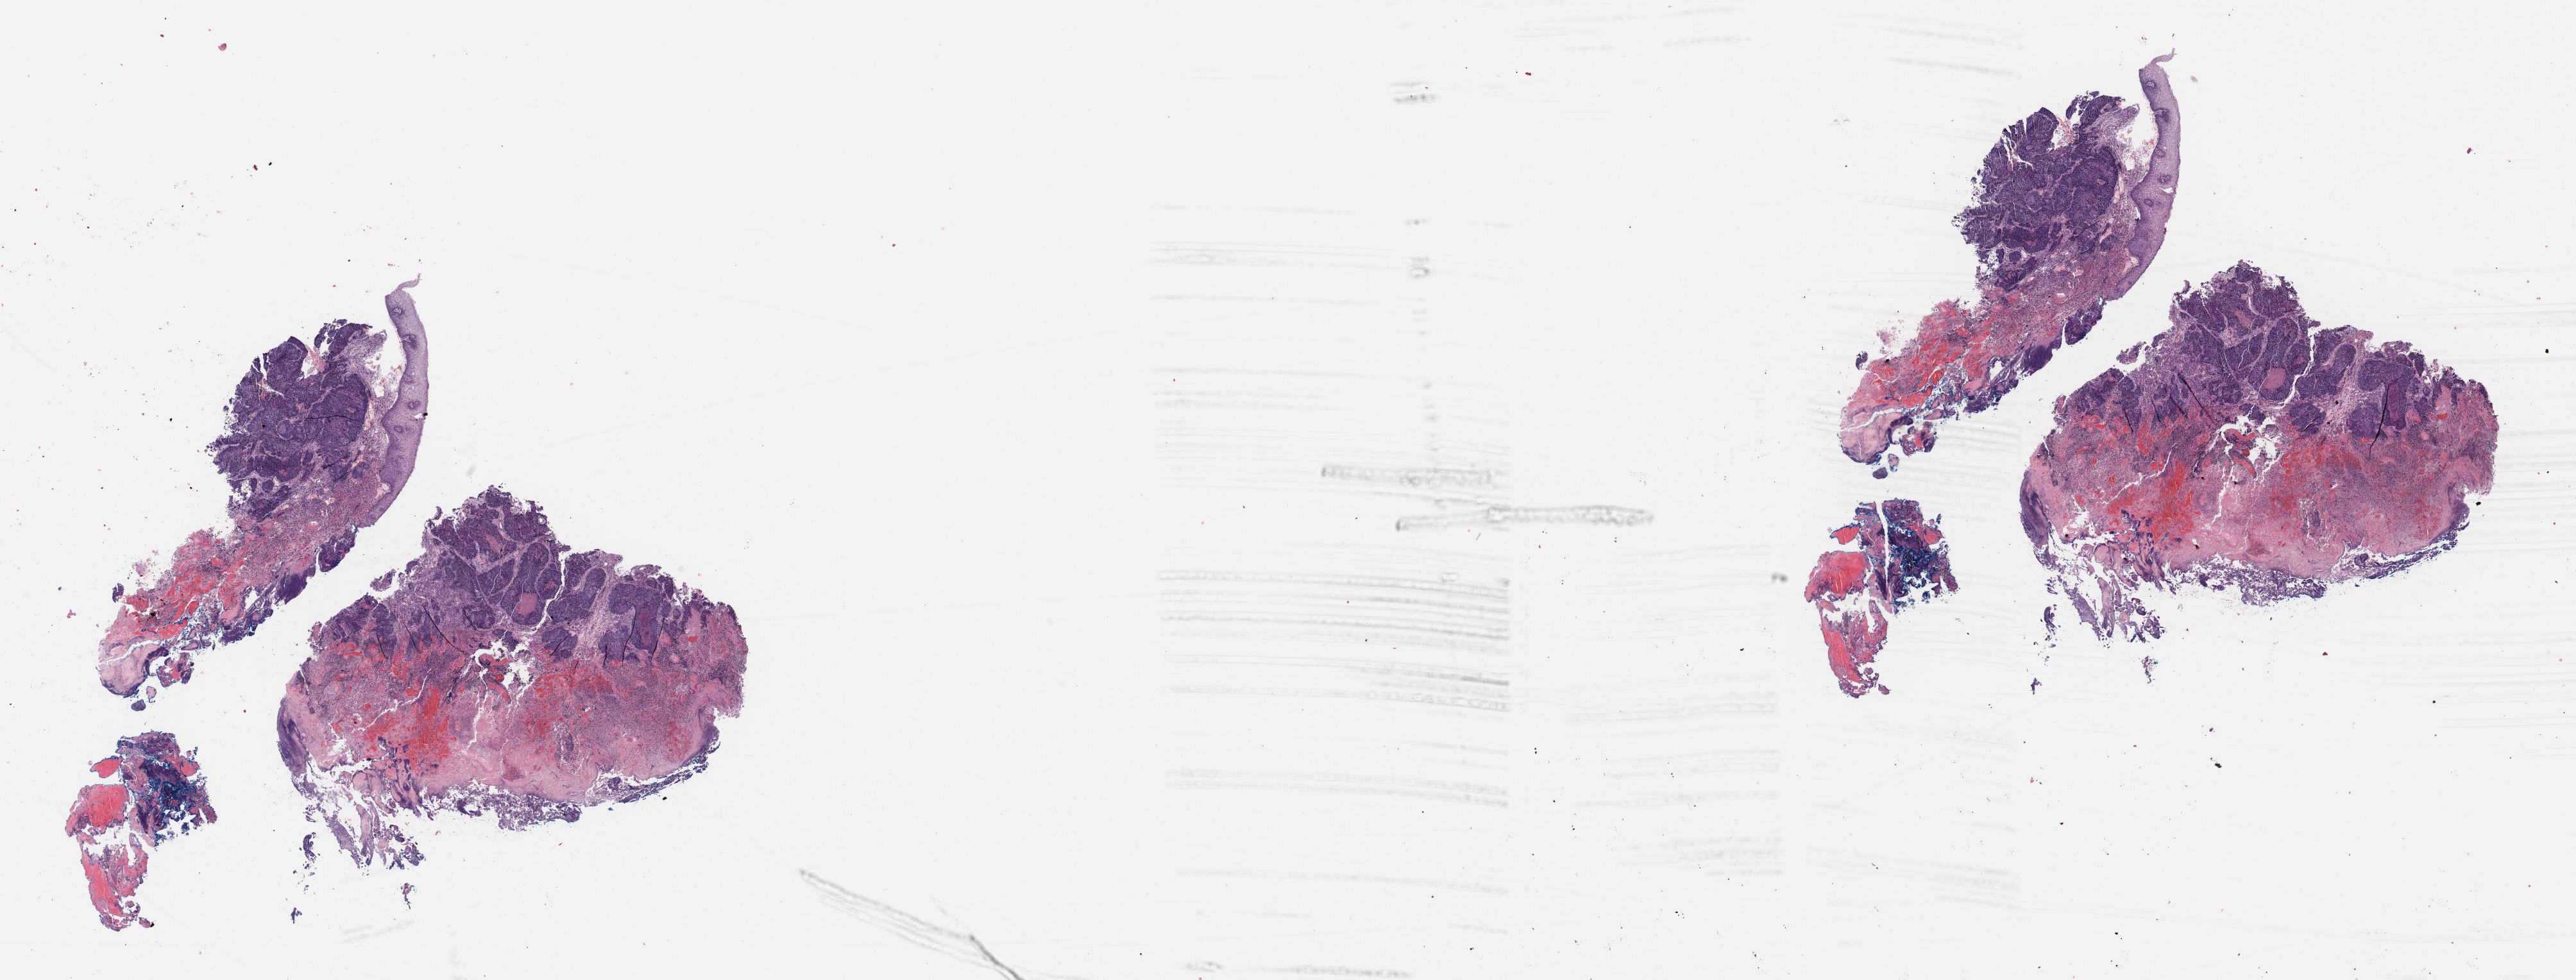
Digitized H&E-stained tissue section (whole slide) — shown as a low-resolution overview of the whole scanned area (about 31.7 x 12.1 mm). Formalin-fixed paraffin-embedded (FFPE) diagnostic section. Sample: primary tumour, cervix. Patient: female, age at initial diagnosis 53 years. Histologic grade: G2 (moderately differentiated).
- histologic diagnosis: Squamous cell carcinoma, NOS (cervix uteri)
- FIGO stage: IVB